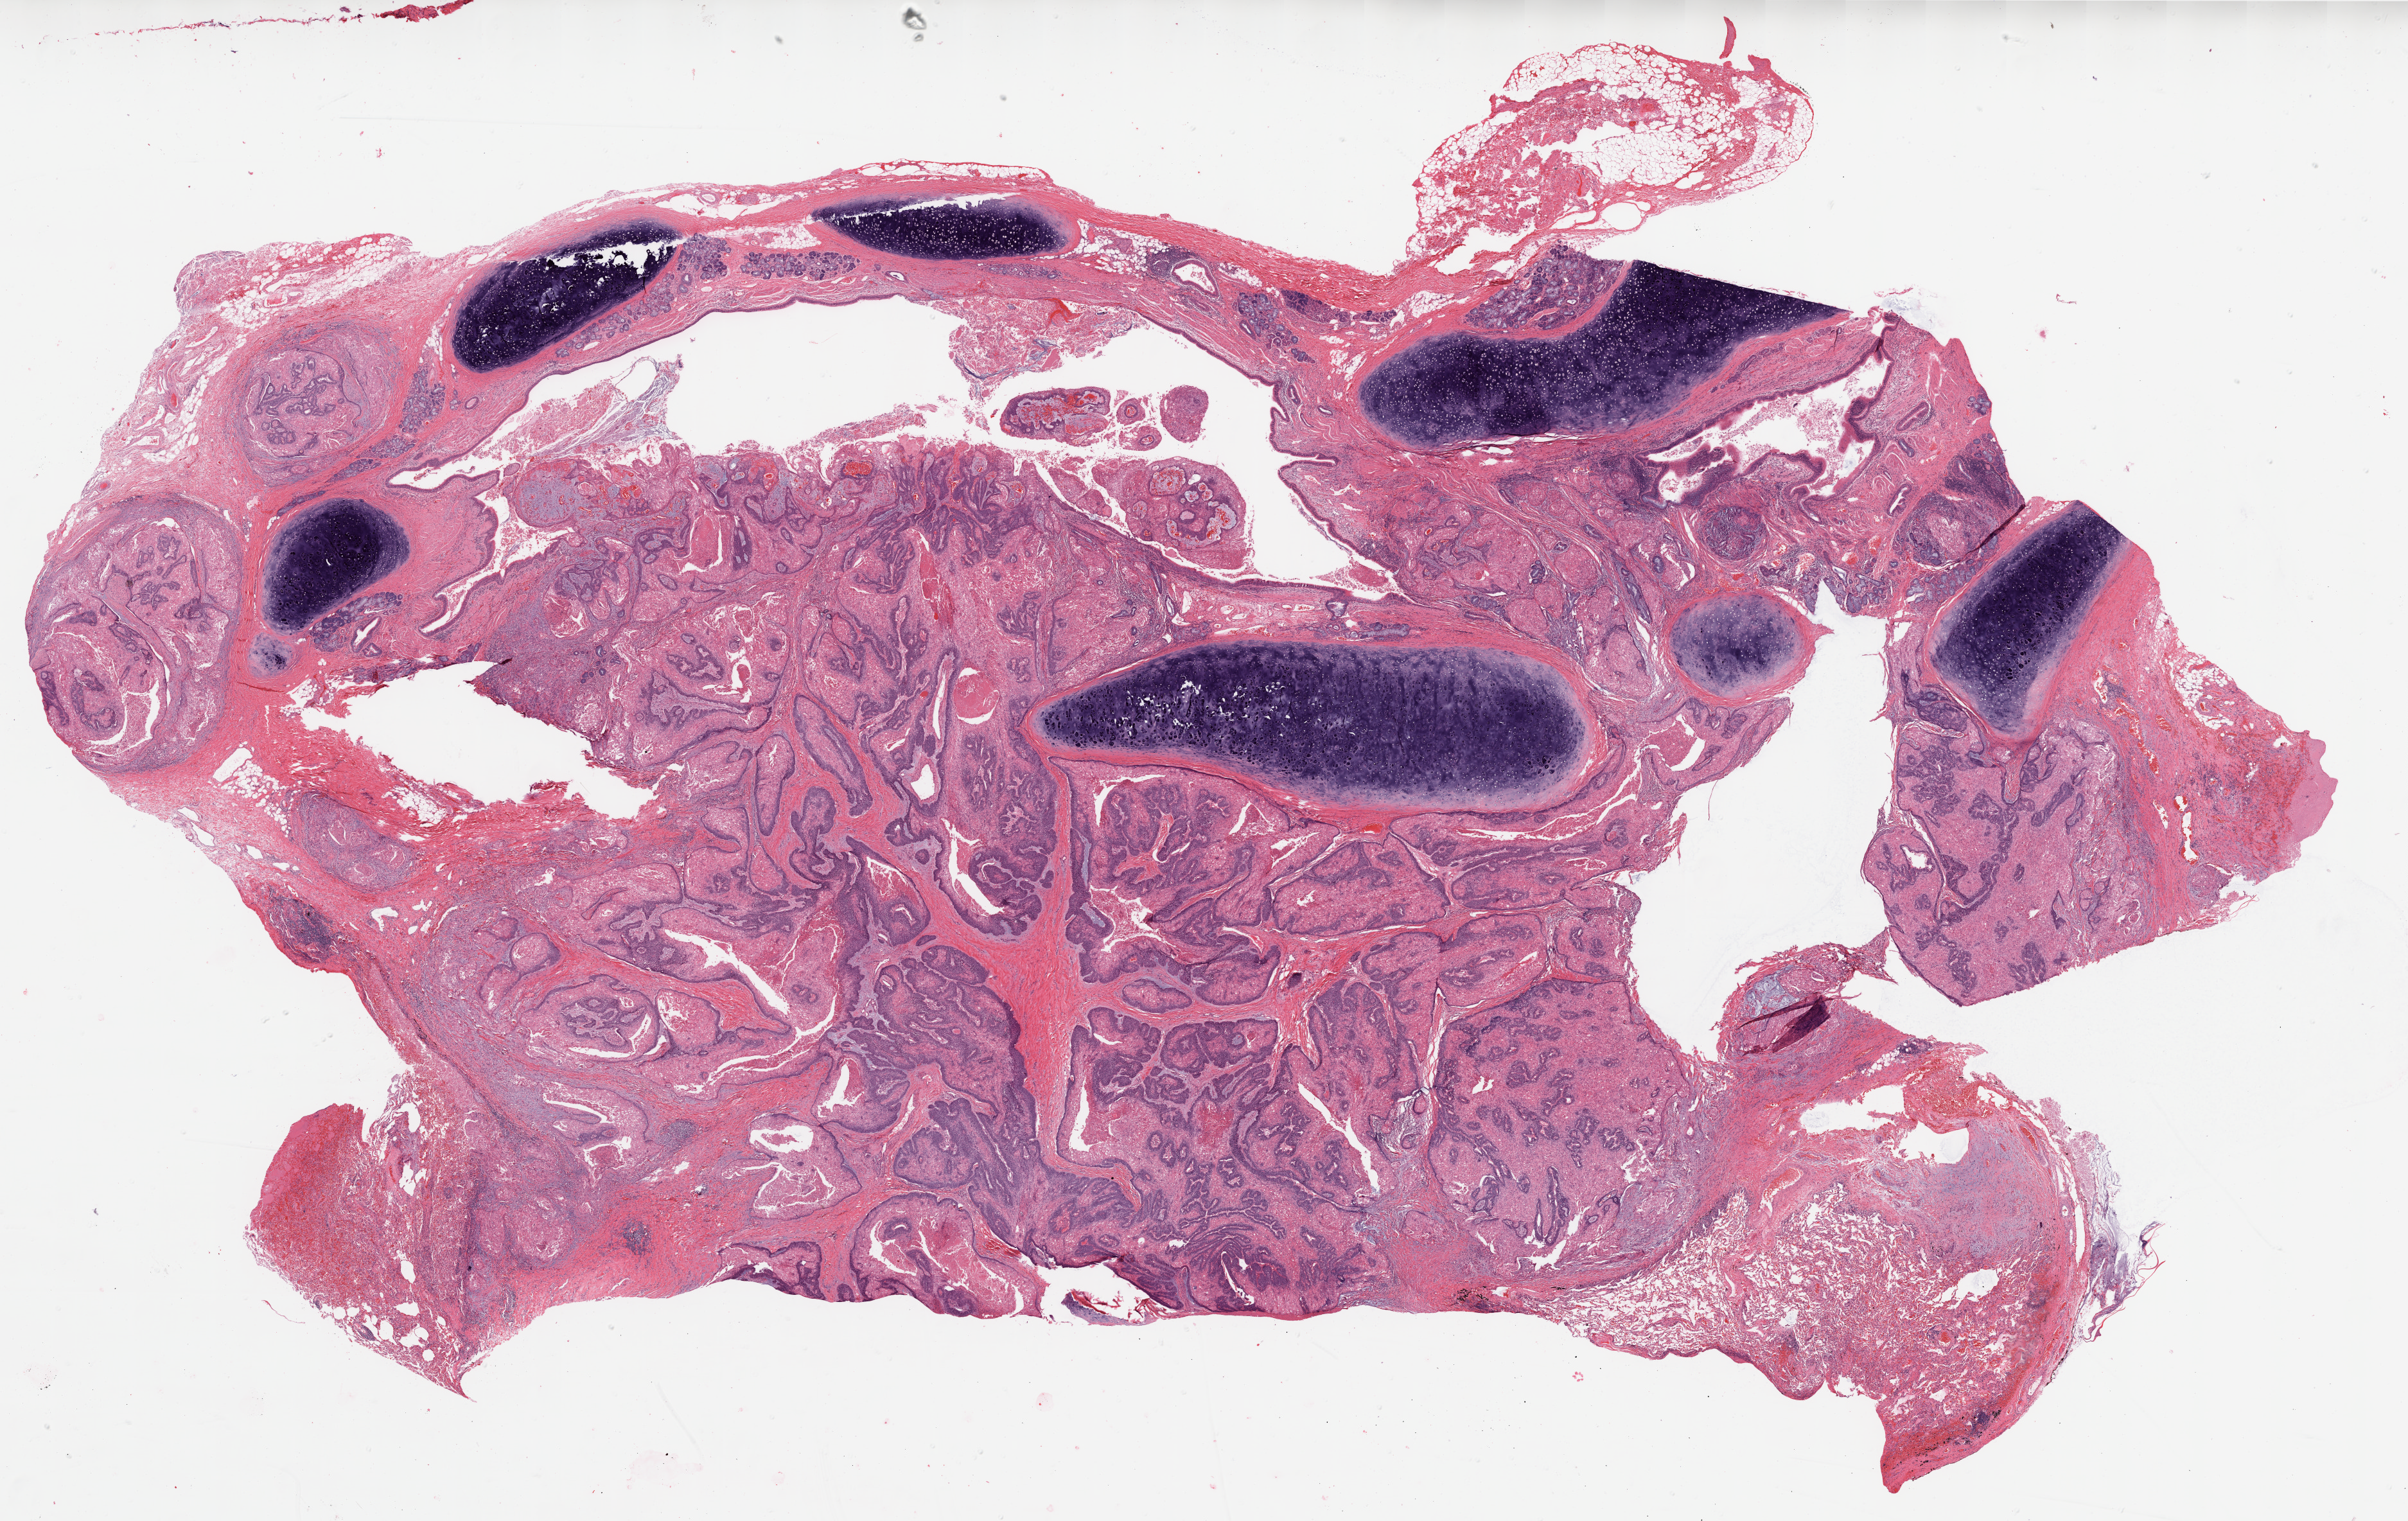
Digitized H&E tissue section (whole slide) — whole scanned area (about 30.1 x 19.0 mm, from a 20x scan) shown as a low-resolution overview. Formalin-fixed paraffin-embedded (FFPE) diagnostic section. Lung, primary tumour sample. Male, age 39 years at initial diagnosis.
Laterality: left. Histologic diagnosis: Squamous cell carcinoma, NOS. AJCC pathologic stage: IIB.